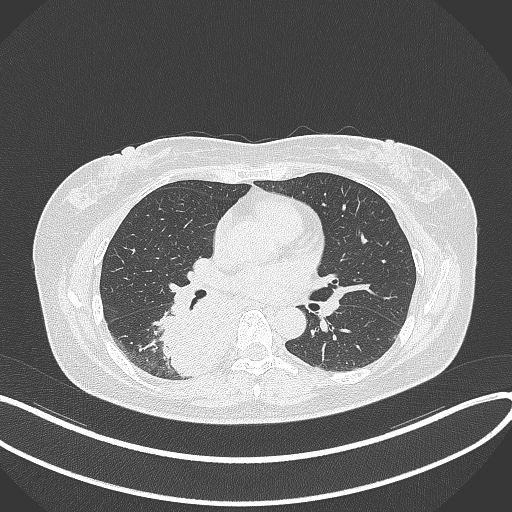
Chest CT, one axial slice. Slice 188 of 331 in the series (ordered by position). Reconstruction kernel B70f. 120 kVp. Lung window (W 1500 / L -600 HU). 1 mm slice thickness. 512 × 512 image matrix, field of view 400 × 400 mm. Patient: female, 54 years. From the clinical record (not read from this slice): clinical TNM (as recorded): T4 N0 M0.
Annotated regions visible in this slice (bounding box drawn by a radiologist):
- lung tumour (recorded histology: adenocarcinoma): bounding box <160,282,232,378> (left, top, right, bottom; pixels)